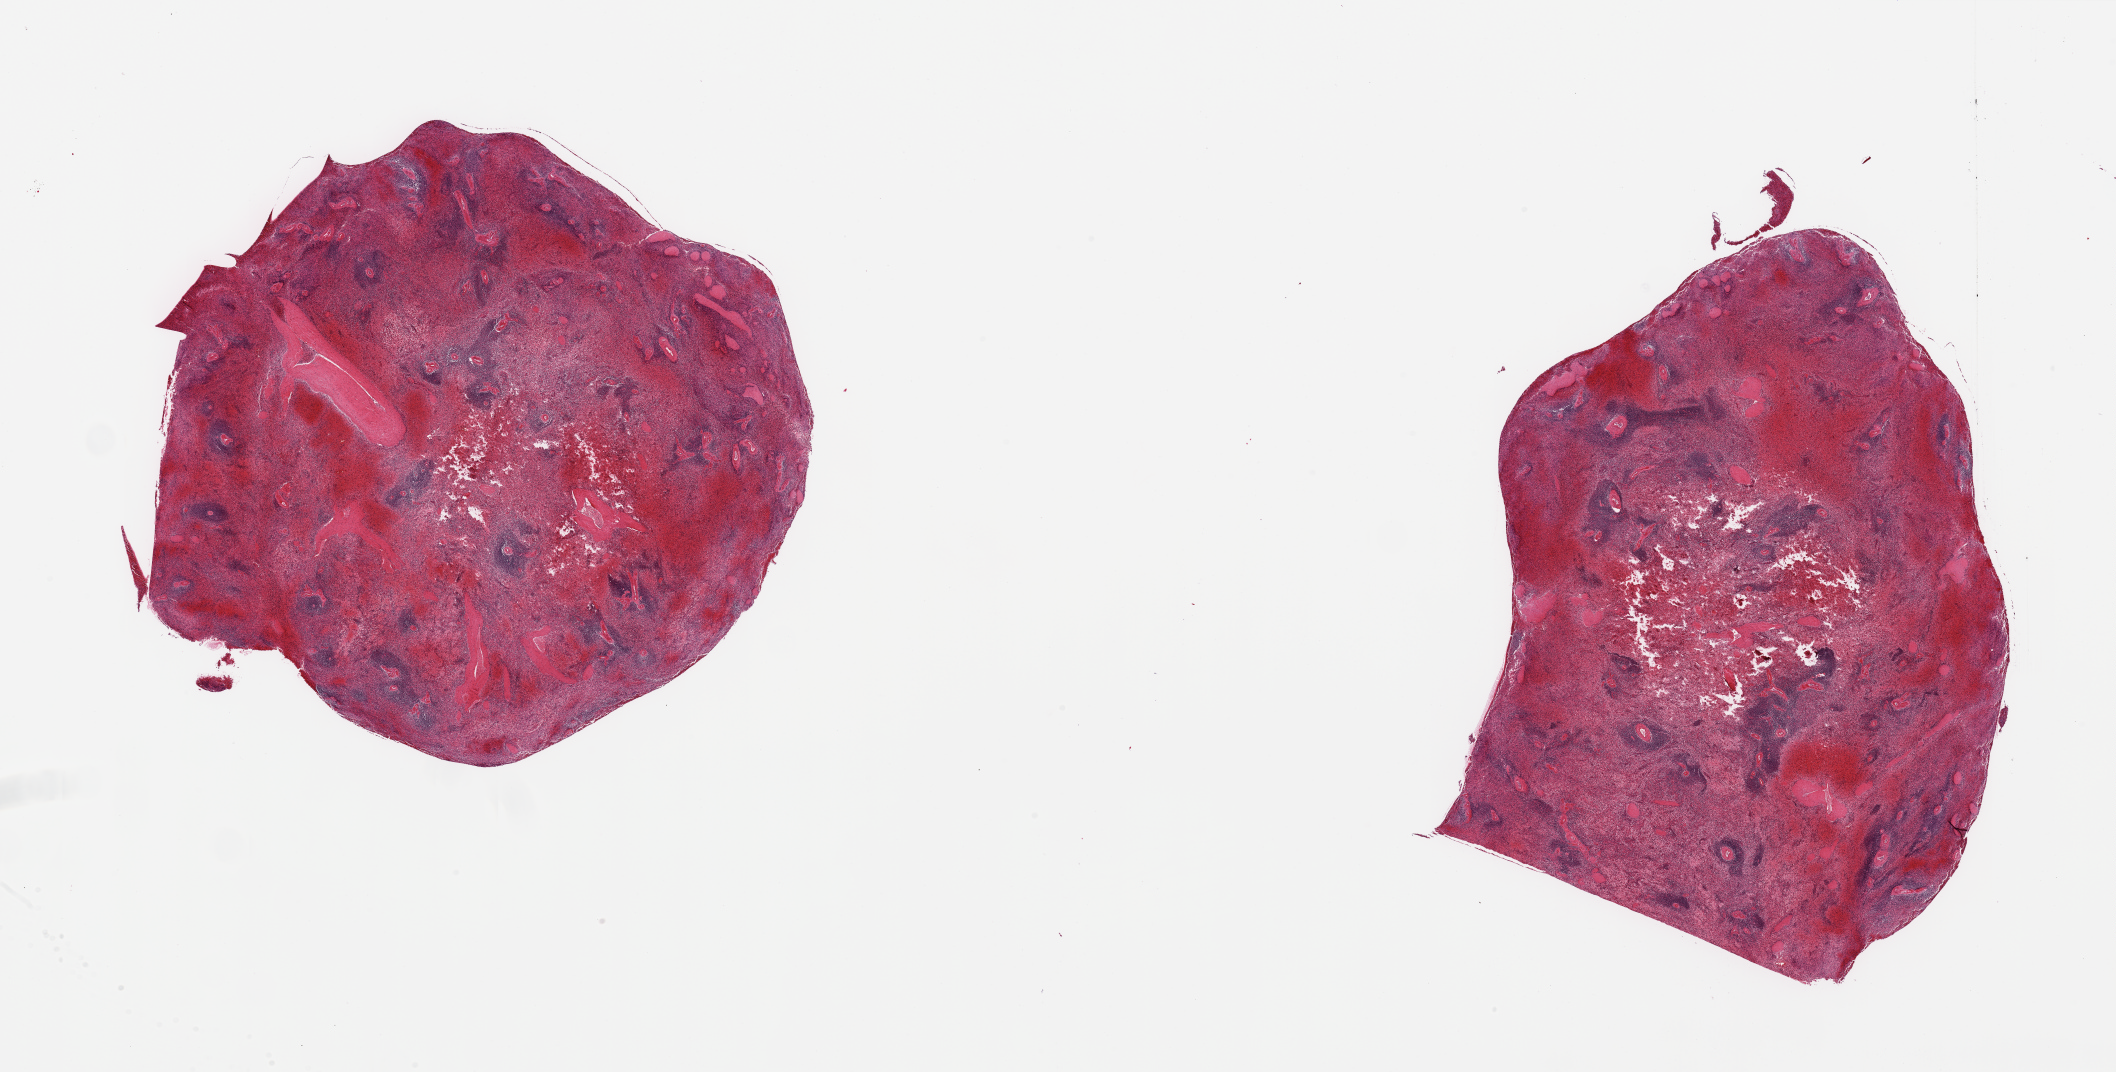
Digitized hematoxylin and eosin (H&E)-stained section, brightfield — whole scanned area (about 33.5 x 17.0 mm) shown as a low-resolution overview, PAXgene-fixed paraffin-embedded (PFPE) section, target tissue: spleen, tissue donor sample. Donor: male.
Review note (as recorded): 2 pieces; heavily congested focally.